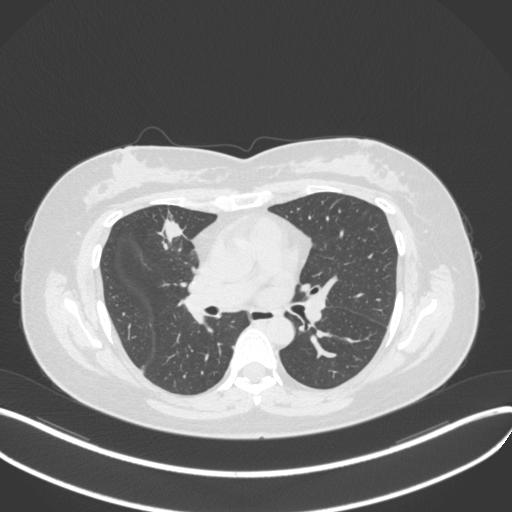
Chest CT, one axial slice. Position 173 of 272 along the scan axis. Lung window (W 1500 / L -600 HU). 1 mm slice thickness. 512 × 512 image matrix, field of view 400 × 400 mm. Patient: female, 42 years. Case-level facts recorded for this patient, not image findings: clinical TNM (as recorded): T1b N0 M0.
Structures marked on this image (rectangle marked by the reading radiologist):
- lung tumour (recorded histology: adenocarcinoma): box from (x=154, y=214) to (x=189, y=254) px